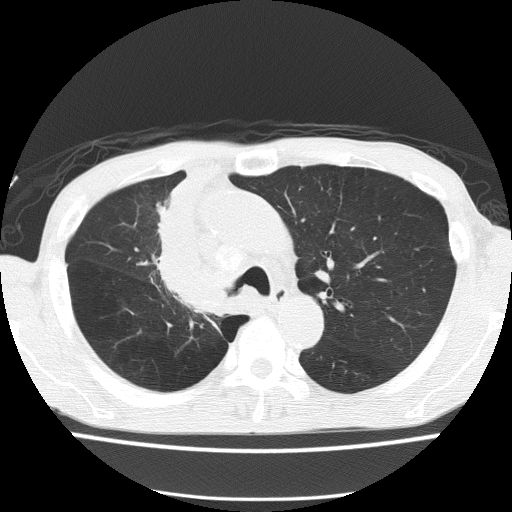
Low-dose screening chest CT, one axial slice; position 103 of 150 along the scan axis; 120 kVp; lung window (W 1500 / L -600 HU); 2 mm slice thickness; 512 × 512 image matrix, field of view 336 × 336 mm.
Structures marked on this image (expert manual segmentation):
- lesion 1 (tumor, hilum of right lung): box from (x=160, y=180) to (x=227, y=313) px